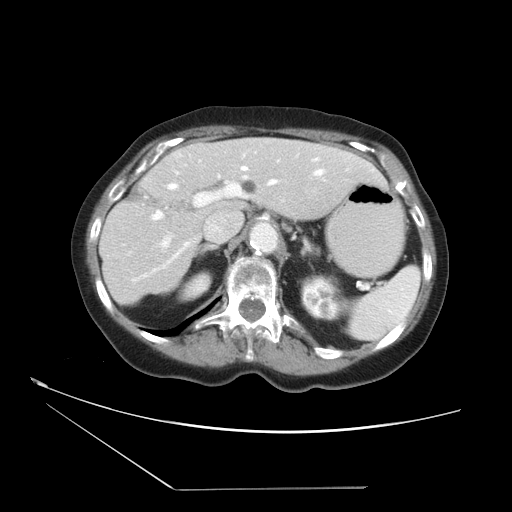
Contrast-enhanced abdominal CT, one axial slice; position 23 of 36 along the scan axis; intravenous contrast given; soft-tissue window (W 400 / L 40 HU); 512 × 512 image matrix, field of view 384 × 384 mm. Female patient, age 81 years. Case-level facts recorded for this patient, not image findings: diagnosis: colorectal cancer liver metastases, imaged before liver resection; multiple liver metastases: no; largest metastasis: 1.6 cm; disease in both lobes: no.
Outlined on this slice (manually delineated by an expert):
- hepatic veins: bounding box [x1, y1, x2, y2] px = [130, 158, 326, 285]
- liver: [99, 138, 387, 306]
- planned liver remnant (the part of the liver to remain after resection): [99, 139, 387, 306]
- portal vein (with intrahepatic branches): [129, 176, 247, 254]
- liver metastasis: [242, 179, 257, 196]